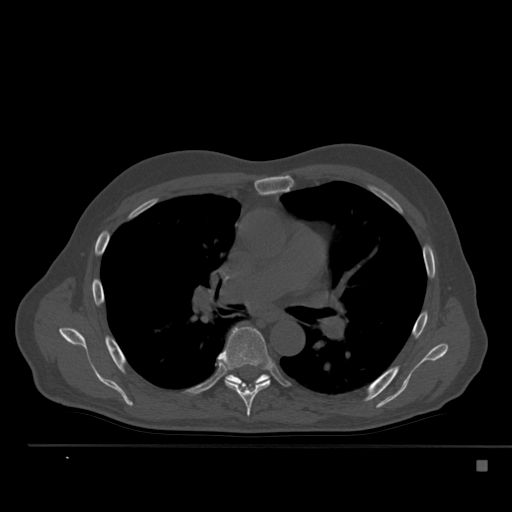
CT including the spine, one axial slice. Position 341 of 517 along the scan axis. Reconstruction kernel Br40s. 120 kVp. Bone window (W 1800 / L 400 HU). 1.5 mm slice thickness. 512 × 512 image matrix. Patient: male, 70 years. From the clinical record (not read from this slice): primary cancer: renal; vertebrae with lytic lesions (as recorded): T4, T6, T10, T12, L3, L4, L5.
Annotated regions visible in this slice (semi-automatic segmentation, software-assisted and operator-edited):
- T6 vertebra: box from (x=219, y=326) to (x=273, y=417) px
- T7 vertebra: (x=225, y=374)–(x=270, y=387)